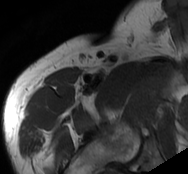
MRI of an extremity soft-tissue mass, one axial slice. Slice 75 of 93 in the series (ordered by position). MR volume resampled by the dataset authors to the PET/CT grid (not the native acquisition matrix). 3.27 mm slice thickness. 188 × 174 image matrix. Male patient. Case-level facts recorded for this patient, not image findings: histological type: undifferentiated - pleiomorphic; grade: high; site of the primary tumour: right thigh.
Structures marked on this image (expert contour drawn on MRI and transferred to this co-registered scan by the dataset authors):
- gross tumour volume including surrounding oedema: box from (x=129, y=65) to (x=169, y=95) px
- gross tumour volume (mass): (x=132, y=76)–(x=155, y=93)